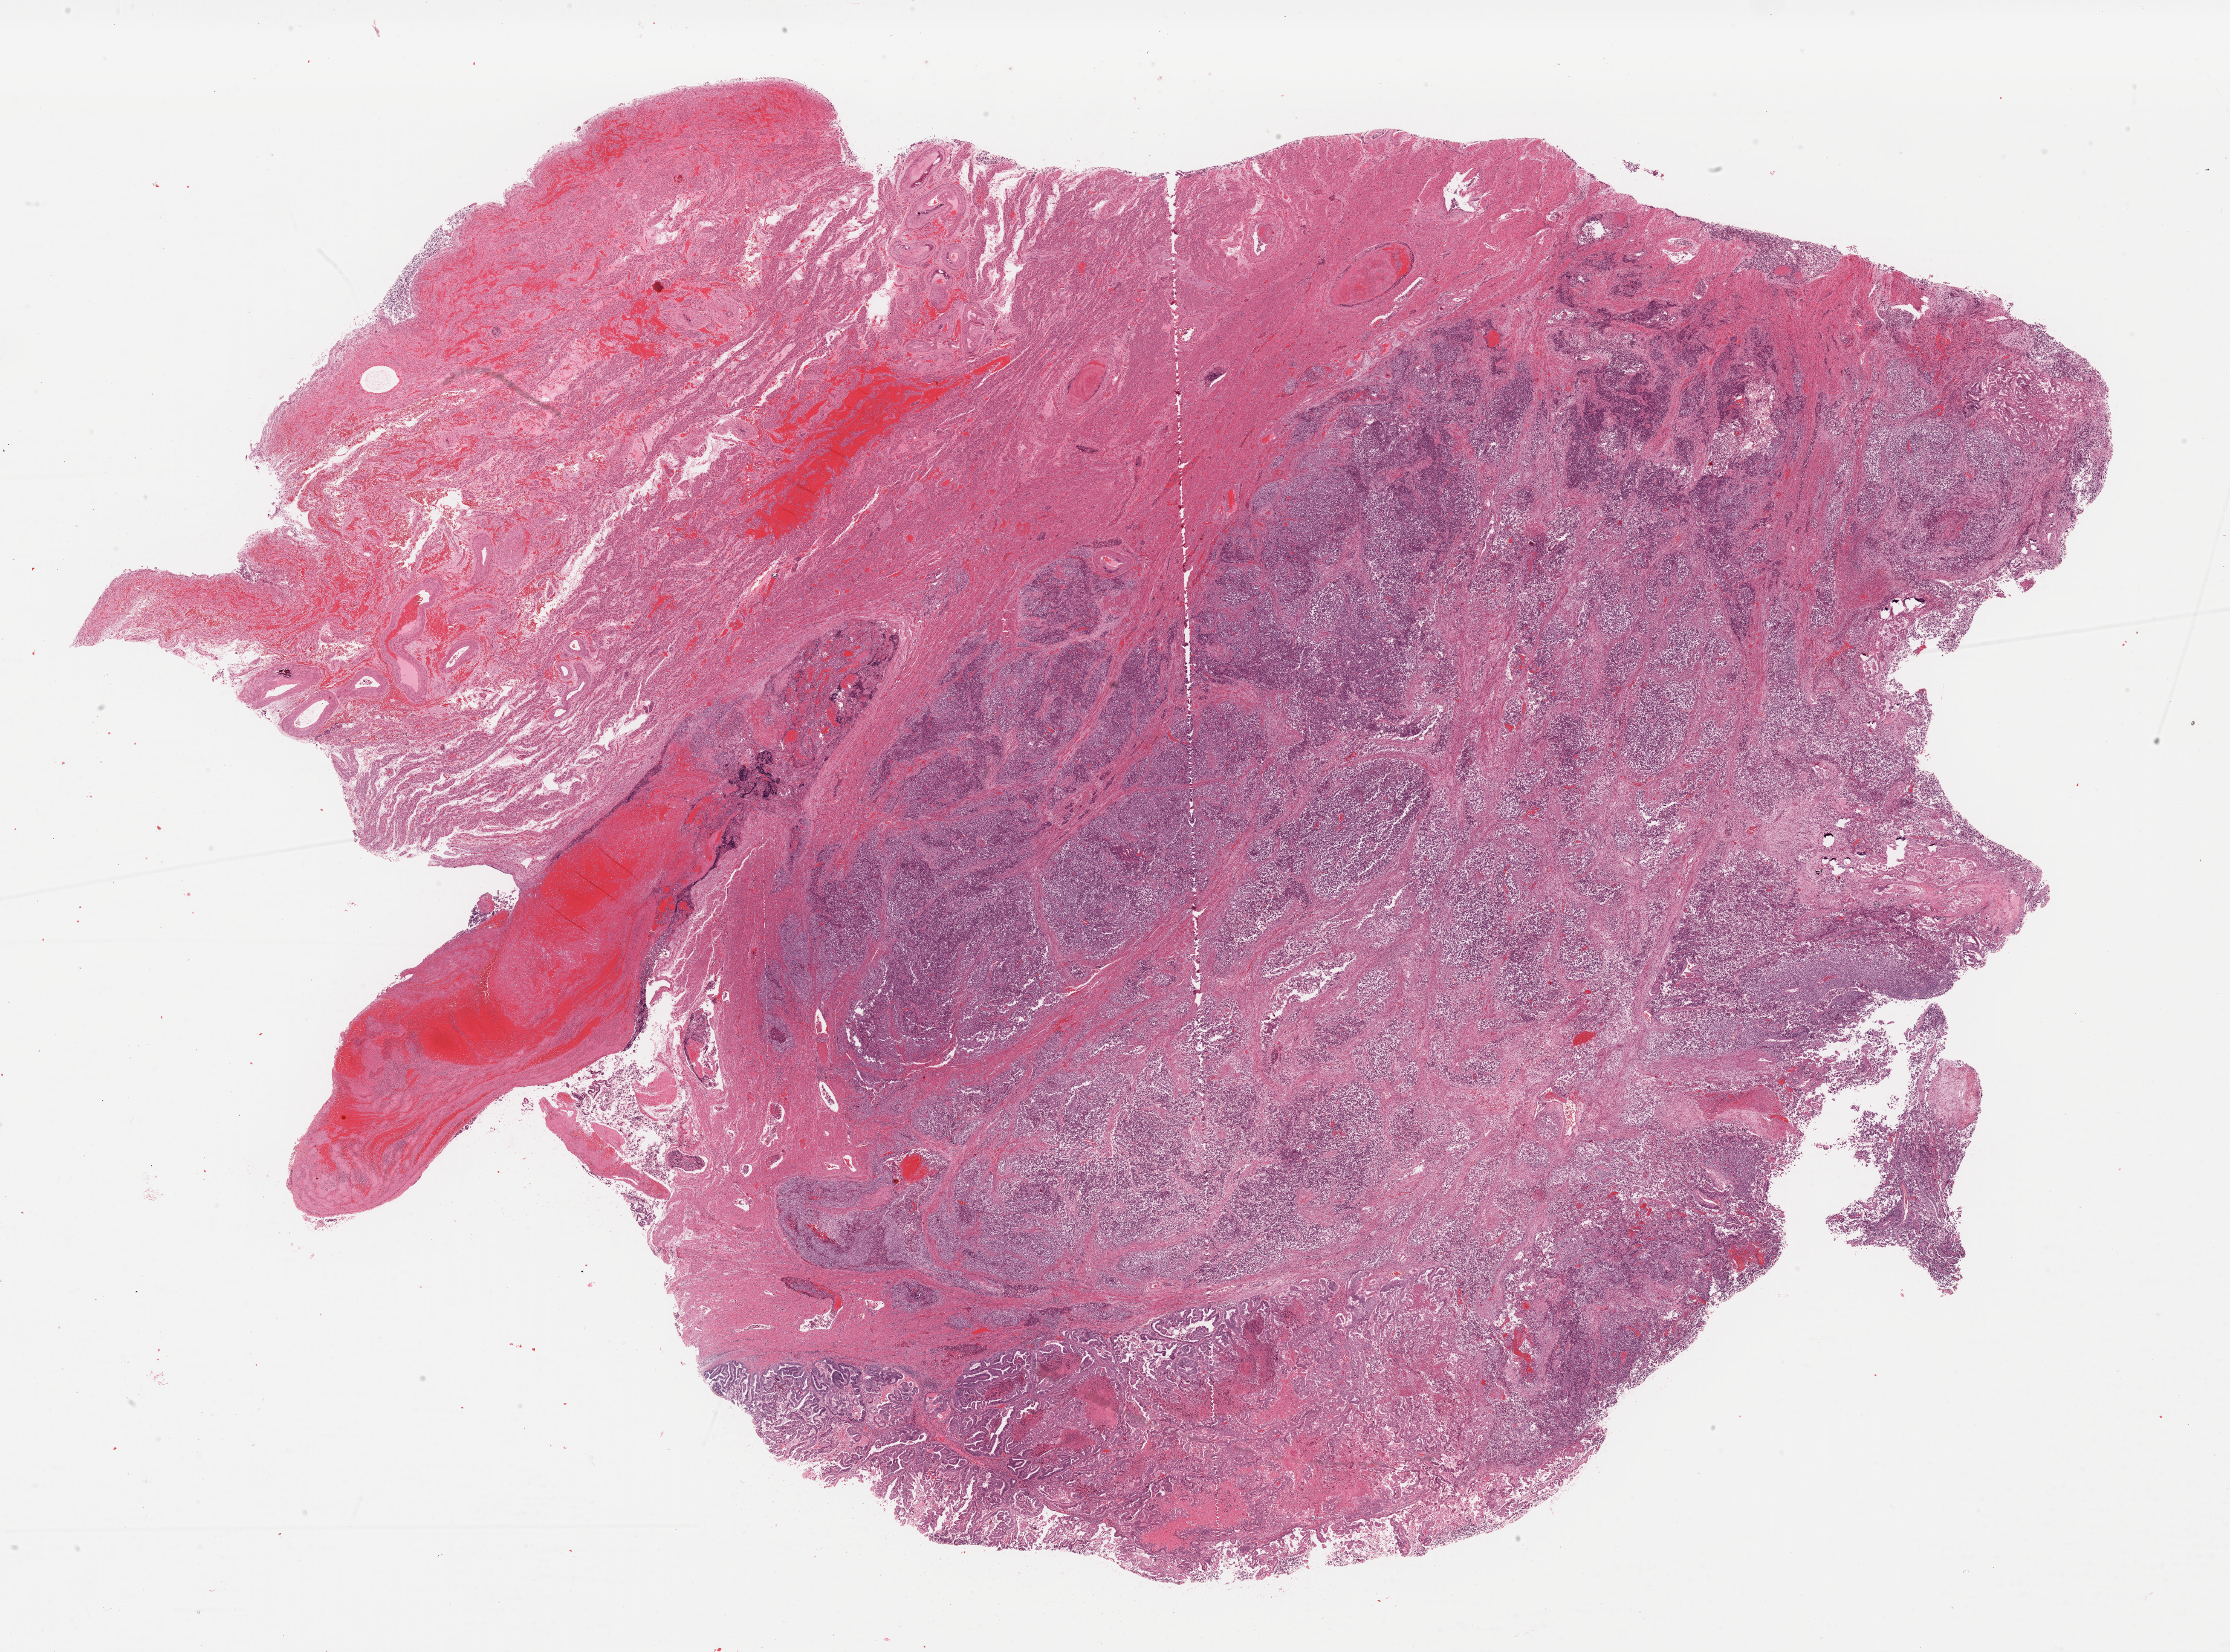
Digitized H&E tissue section (whole slide) — a low-resolution overview of the entire scanned area, about 29.1 x 21.6 mm (acquisition: 40x scan); formalin-fixed paraffin-embedded (FFPE) diagnostic section; sample: primary tumour, uterus. Patient: female, age at initial diagnosis 82 years. Histologic grade: G2 (moderately differentiated).
- FIGO stage: IIIA
- diagnosis: Endometrioid adenocarcinoma, NOS (endometrium)